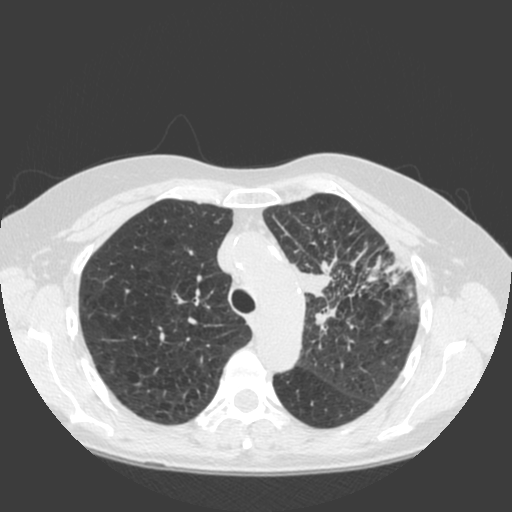
Chest CT (low-dose screening protocol), one axial image. Baseline screening round. Lung window (W 1500 / L -600 HU). 2 mm slice thickness. Female participant, aged 66 years at enrolment.
• Lesion marked by an expert reader, bounding box (x1, y1, x2, y2) in pixels: (286, 245, 396, 343).
• Screening reader's record for this exam (one nodule recorded; not confirmed to be the boxed lesion): non-calcified nodule or mass ≥4 mm, left upper lobe, 61 × 45 mm, spiculated (stellate) margins, soft tissue attenuation.